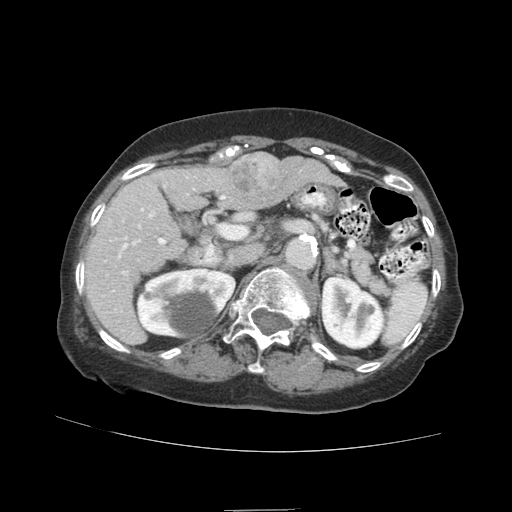
Contrast-enhanced abdominal CT (liver protocol), one axial slice. Slice 50 of 89 in the series (ordered by position). Reconstruction kernel STANDARD. 140 kVp. Soft-tissue window (W 400 / L 40 HU). 2.5 mm slice thickness. 512 × 512 image matrix, field of view 360 × 360 mm. From the clinical record (not read from this slice): diagnosis: hepatocellular carcinoma (patient treated with transarterial chemoembolisation; whether this scan precedes or follows treatment is not stated here); TNM stage (as recorded): Stage-II; Child-Pugh class: A; tumour differentiation: moderately differentiated; tumour nodularity: multinodular.
Outlined on this slice (semi-automatic segmentation, software-assisted and operator-edited):
- liver parenchyma outside the tumour (the mass and vessels are separate outlines, so this box may not span the whole liver): bounding box [x1, y1, x2, y2] px = [84, 160, 341, 344]
- mass: [228, 152, 288, 208]
- liver vessels: [102, 176, 196, 332]